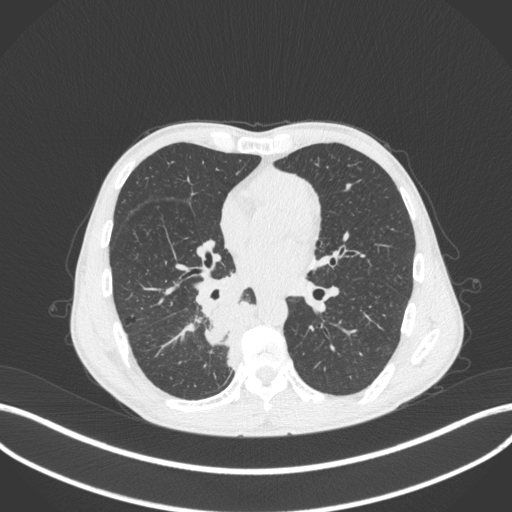
Chest CT, one axial slice. Slice 182 of 371 in the series (ordered by position). 120 kVp. Lung window (W 1500 / L -600 HU). 1 mm slice thickness. 512 × 512 image matrix, field of view 400 × 400 mm. Patient: male, 58 years. Case-level facts recorded for this patient, not image findings: clinical TNM (as recorded): T3 N1 M1.
Structures marked on this image (rectangle marked by the reading radiologist):
- lung tumour (recorded histology: squamous cell carcinoma): box from (x=196, y=295) to (x=259, y=365) px